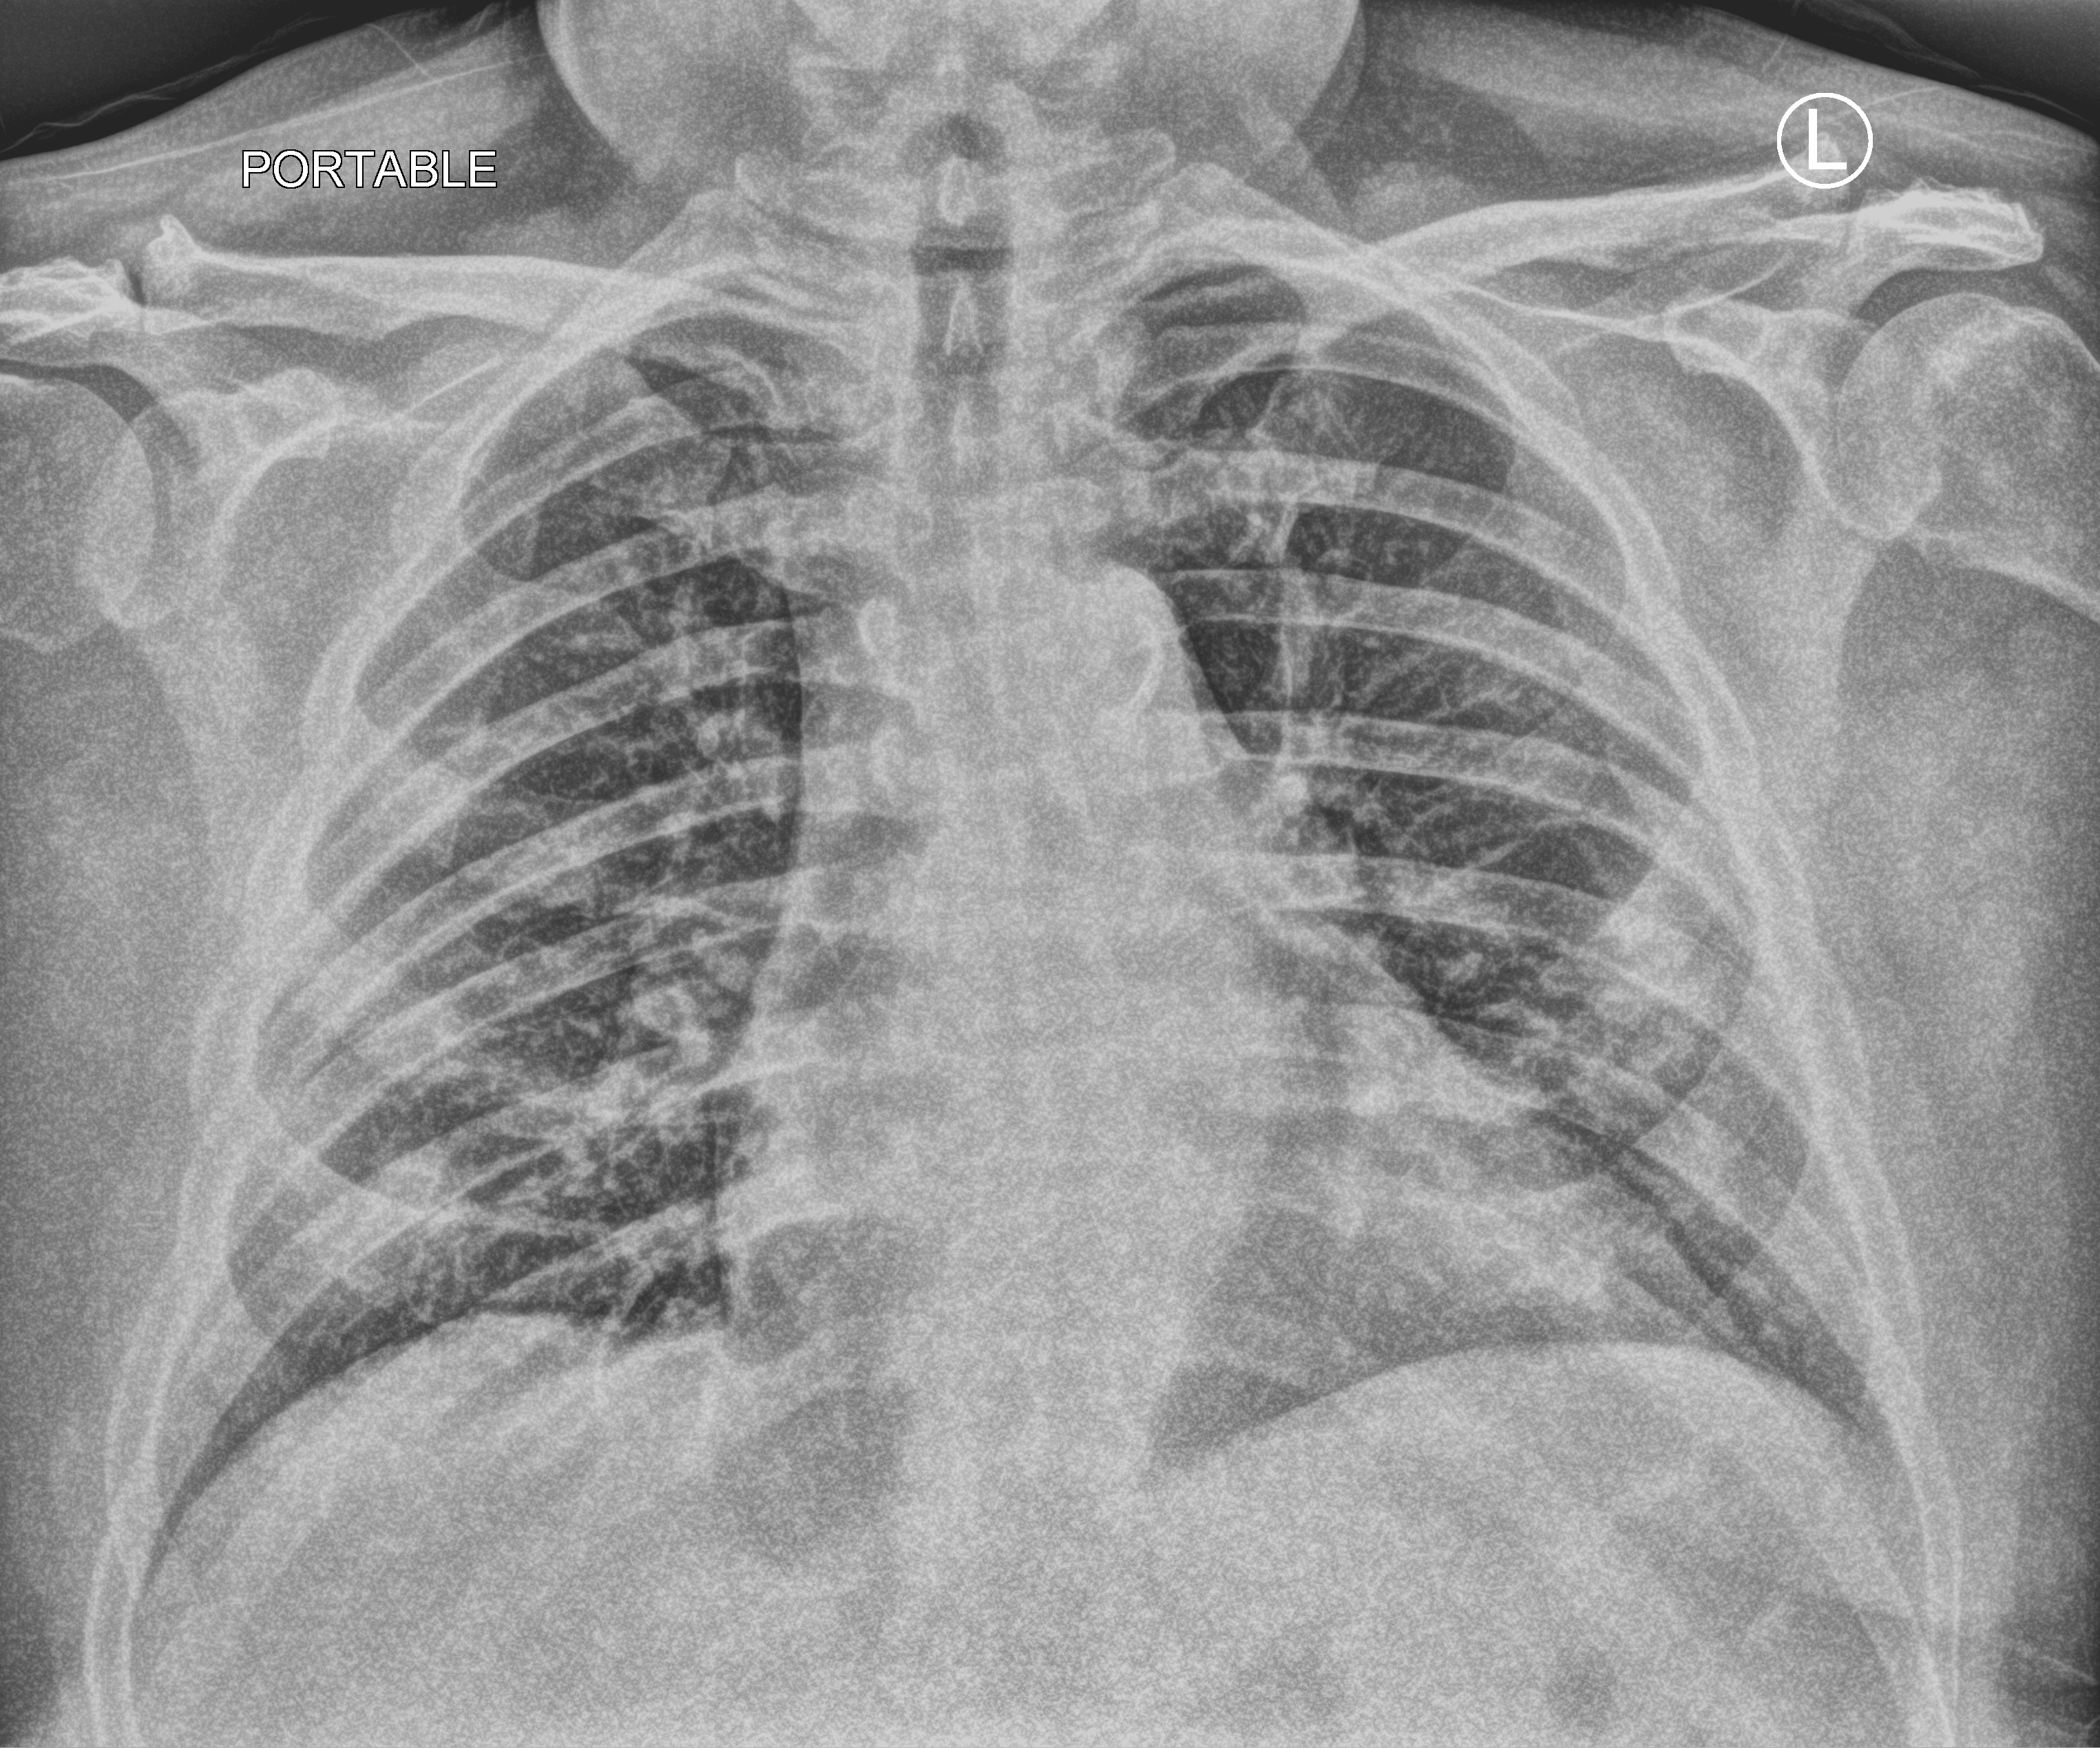
Chest X-ray (portable), anteroposterior (AP) projection. Patient hospitalised with COVID-19; male, aged 18–59 years.
From the hospital-stay record, not from the radiograph (when in the stay this image was taken is not recorded):
- chronic kidney disease (admission record): no
- length of hospital stay: 3 days